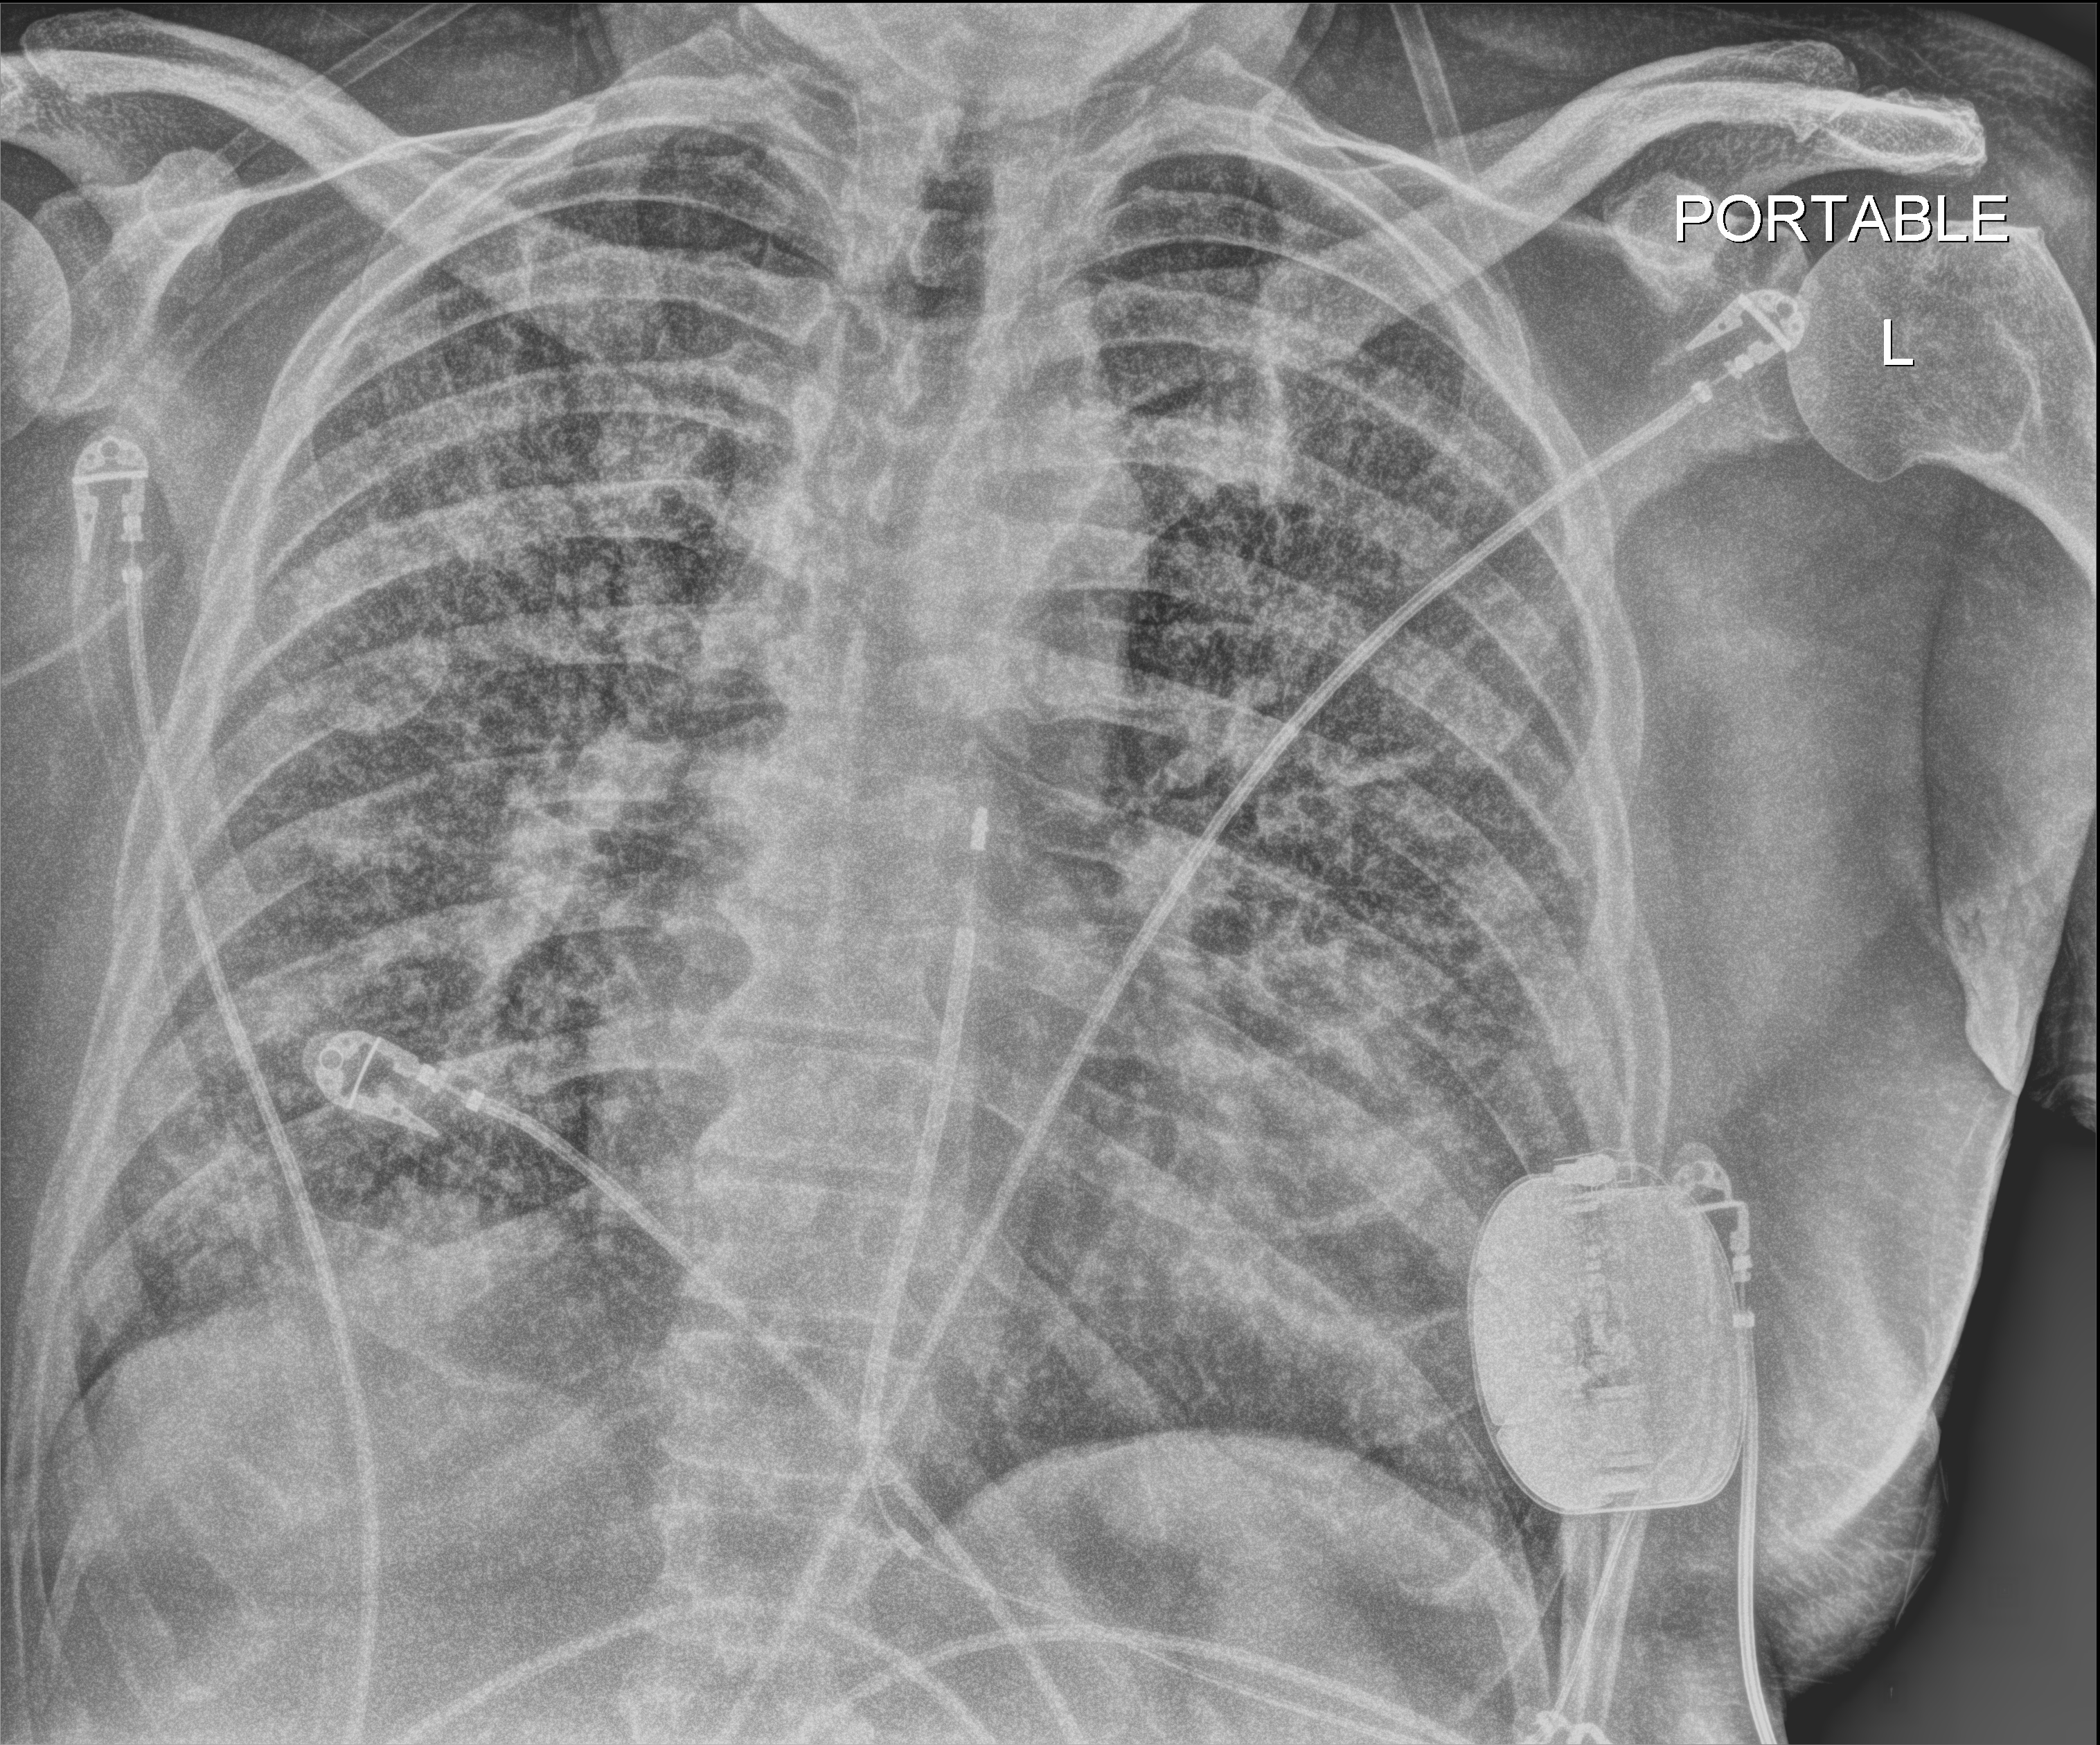
Portable chest radiograph. Male patient hospitalised with COVID-19, age 60–74 years.
Hospital-stay facts (about this admission, not read from this image; timing relative to this image not recorded):
- mechanically ventilated during this hospital stay: yes
- smoking status (admission record): never